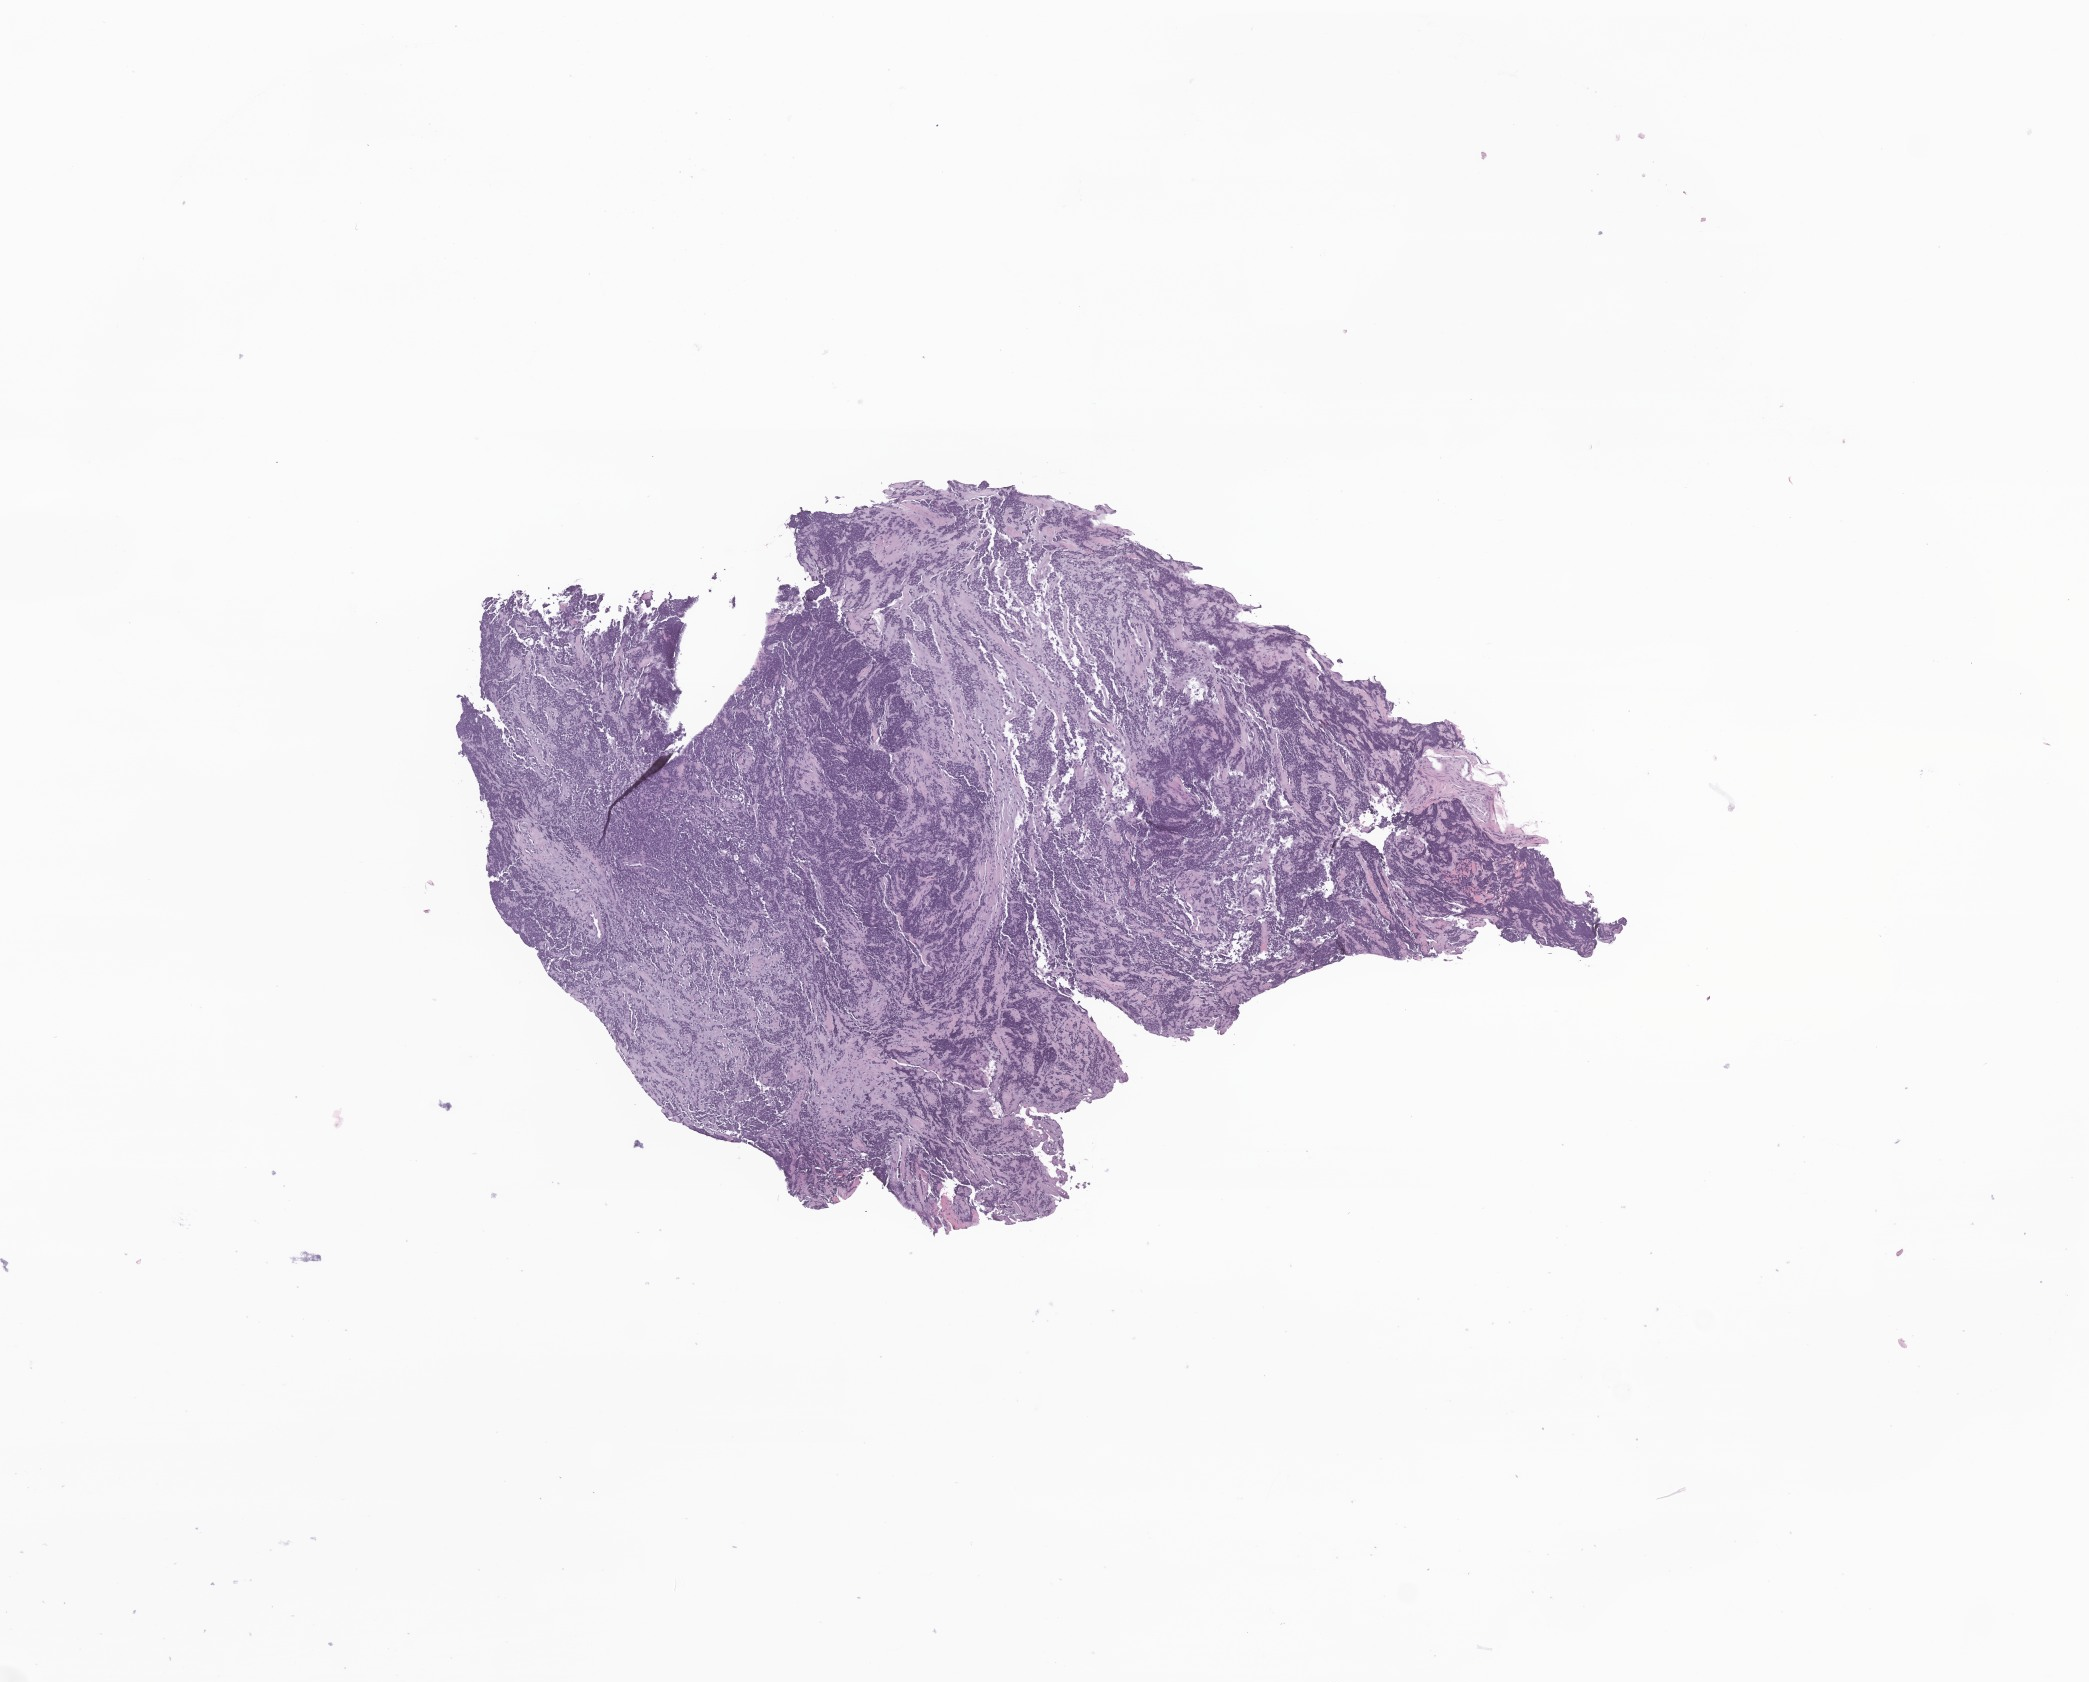
H&E whole-slide image of tumor tissue from the soft tissues of head and neck — shown as a low-resolution overview of the whole scanned area (about 8.8 x 7.1 mm), formalin-fixed, paraffin-embedded (FFPE) tissue. Patient: male, age 657 days (about 1.8 years).
Tissue or organ of origin (case record): connective, subcutaneous and other soft tissues of head, face, and neck. Recorded diagnosis: Alveolar rhabdomyosarcoma.